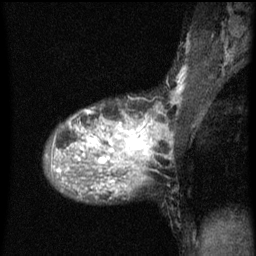
Breast MRI (dynamic contrast-enhanced), one sagittal slice; slice 37 of 60 in the series (ordered by position); dynamic contrast-enhanced series, image 2 of 3 at this slice position (ordered by acquisition); 1.5 T; TE 4.2 ms, TR 8 ms; 2 mm slice thickness; 256 × 256 image matrix, field of view 180 × 180 mm. Patient: female, 36 years.
Structures marked on this image (semi-automatically segmented with operator editing):
- analysis volume of interest (the breast-tissue region the enhancement analysis was run in; not a lesion): box from (x=48, y=110) to (x=167, y=161) px
- tumour enhancement mask (voxels above the 70 % enhancement threshold inside the analysis volume of interest): (x=52, y=114)–(x=155, y=161)